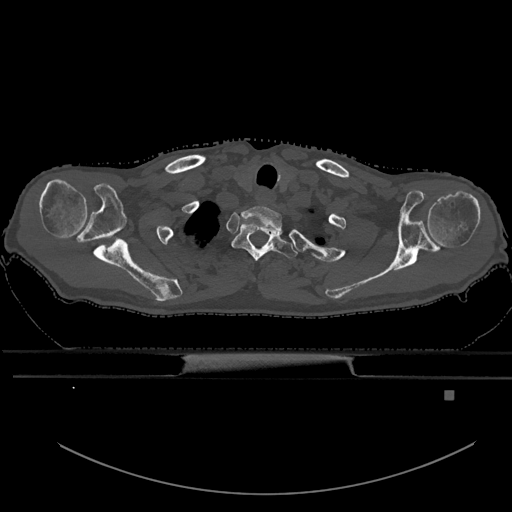
CT including the spine, one axial slice. Position 543 of 969 along the scan axis. Bone window (W 1800 / L 400 HU). 512 × 512 image matrix, field of view 456 × 456 mm. Male patient, age 82 years. From the clinical record (not read from this slice): primary cancer: prostate; vertebrae with lytic lesions (as recorded): T11, T9, T8, T2.
Structures marked on this image (semi-automatically segmented with operator editing):
- T1 vertebra: bounding box (x1, y1, x2, y2) in pixels: (232, 224, 297, 262)